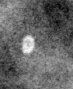
Region of interest cut from a scanned film mammogram (one marked finding), right breast, CC view, BI-RADS breast density category 2 (scale 1–4).
Marked abnormality: calcifications, morphology lucent center; BI-RADS assessment category 2; subtlety rating 3 on a 1 (subtle) to 5 (obvious) scale; benign; no additional work-up was recommended (benign without callback).